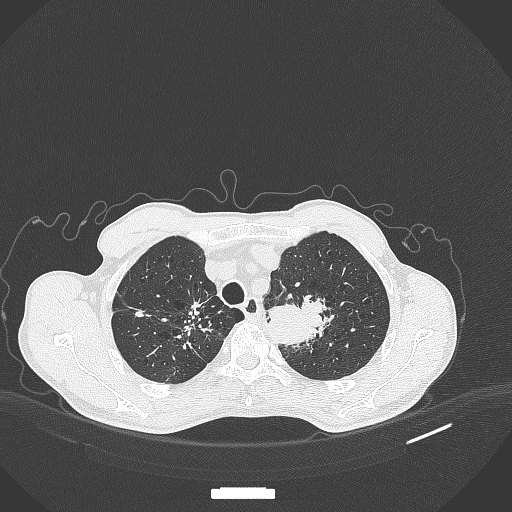
Chest CT, one axial slice; position 352 of 386 along the scan axis; reconstruction kernel B70f; 120 kVp; lung window (W 1500 / L -600 HU); 1 mm slice thickness; 512 × 512 image matrix, field of view 400 × 400 mm. Patient: male, 65 years. Case-level facts recorded for this patient, not image findings: clinical TNM (as recorded): T2b N0 M0; histopathological grade: G2.
Annotated regions visible in this slice (rectangle marked by the reading radiologist):
- lung tumour (recorded histology: adenocarcinoma): bounding box <265,288,333,350> (left, top, right, bottom; pixels)